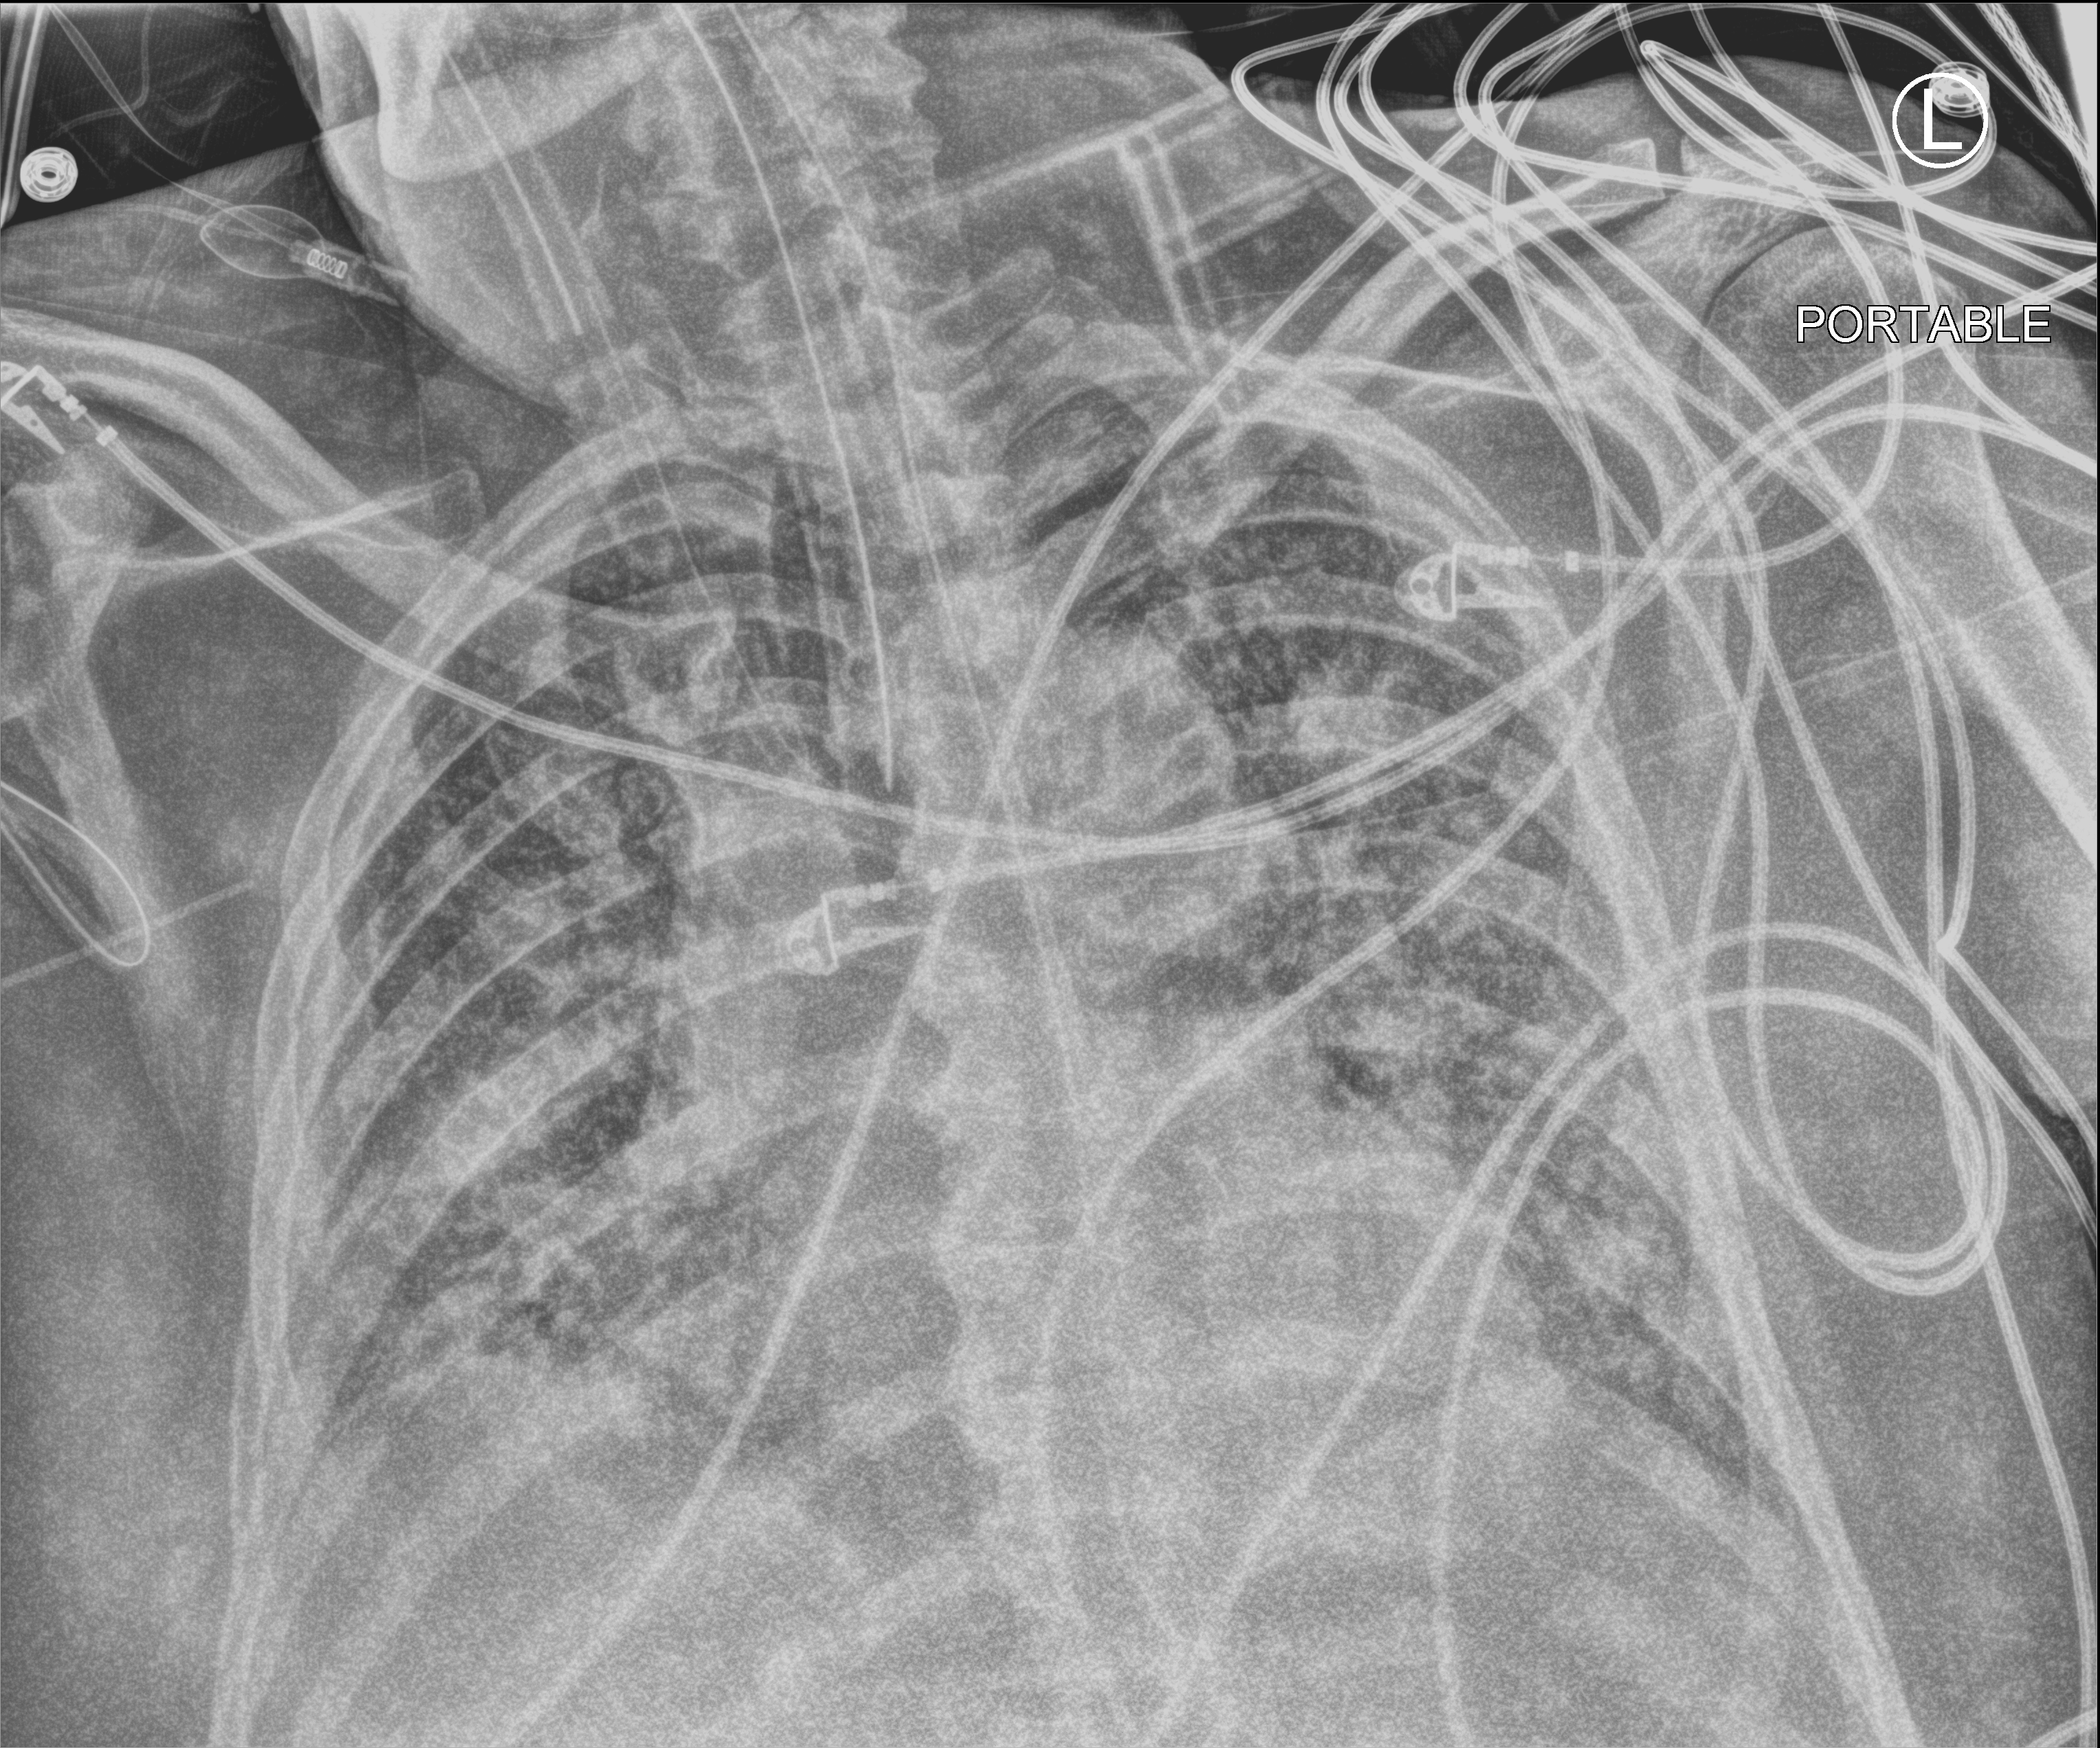
Portable chest radiograph. Male patient hospitalised with COVID-19, age 60–74 years.
Hospital-stay facts (about this admission, not read from this image; timing relative to this image not recorded):
- mechanically ventilated during this hospital stay: yes